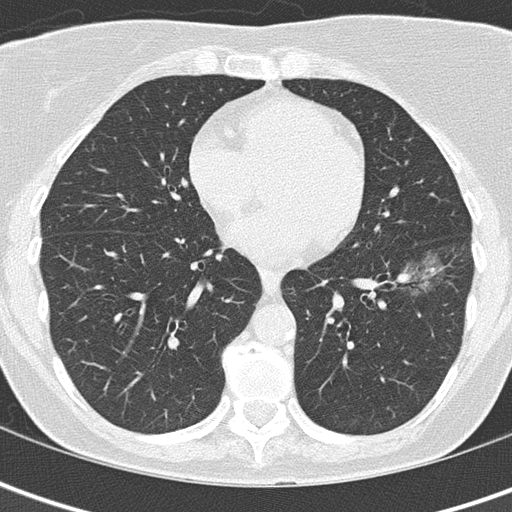
Axial slice from a low-dose chest CT screening exam. Baseline annual screen. Lung window (W 1500 / L -600 HU). 120 kVp. Slice 88 of 149 in the series. 512 × 512 image matrix. Female participant, aged 61 years at enrolment. Former smoker at enrolment.
- Lesion marked by an expert reader, bounding box [x1, y1, x2, y2] px = [381, 248, 456, 306].
- Screening reader's record for this exam (one nodule recorded; not confirmed to be the boxed lesion): non-calcified nodule or mass ≥4 mm, left lower lobe, 29 × 16 mm, ground glass attenuation.
- Official screen result: positive, change unspecified: nodule(s) >= 4 mm or enlarging nodule(s), mass(es), or other non-specific abnormalities suspicious for lung cancer.
- Later outcome: lung cancer diagnosed 259 days after this screen — bronchiolo-alveolar adenocarcinoma, NOS, left lower lobe, well differentiated (G1), stage IA (AJCC 6th edition), 10 mm at pathology.